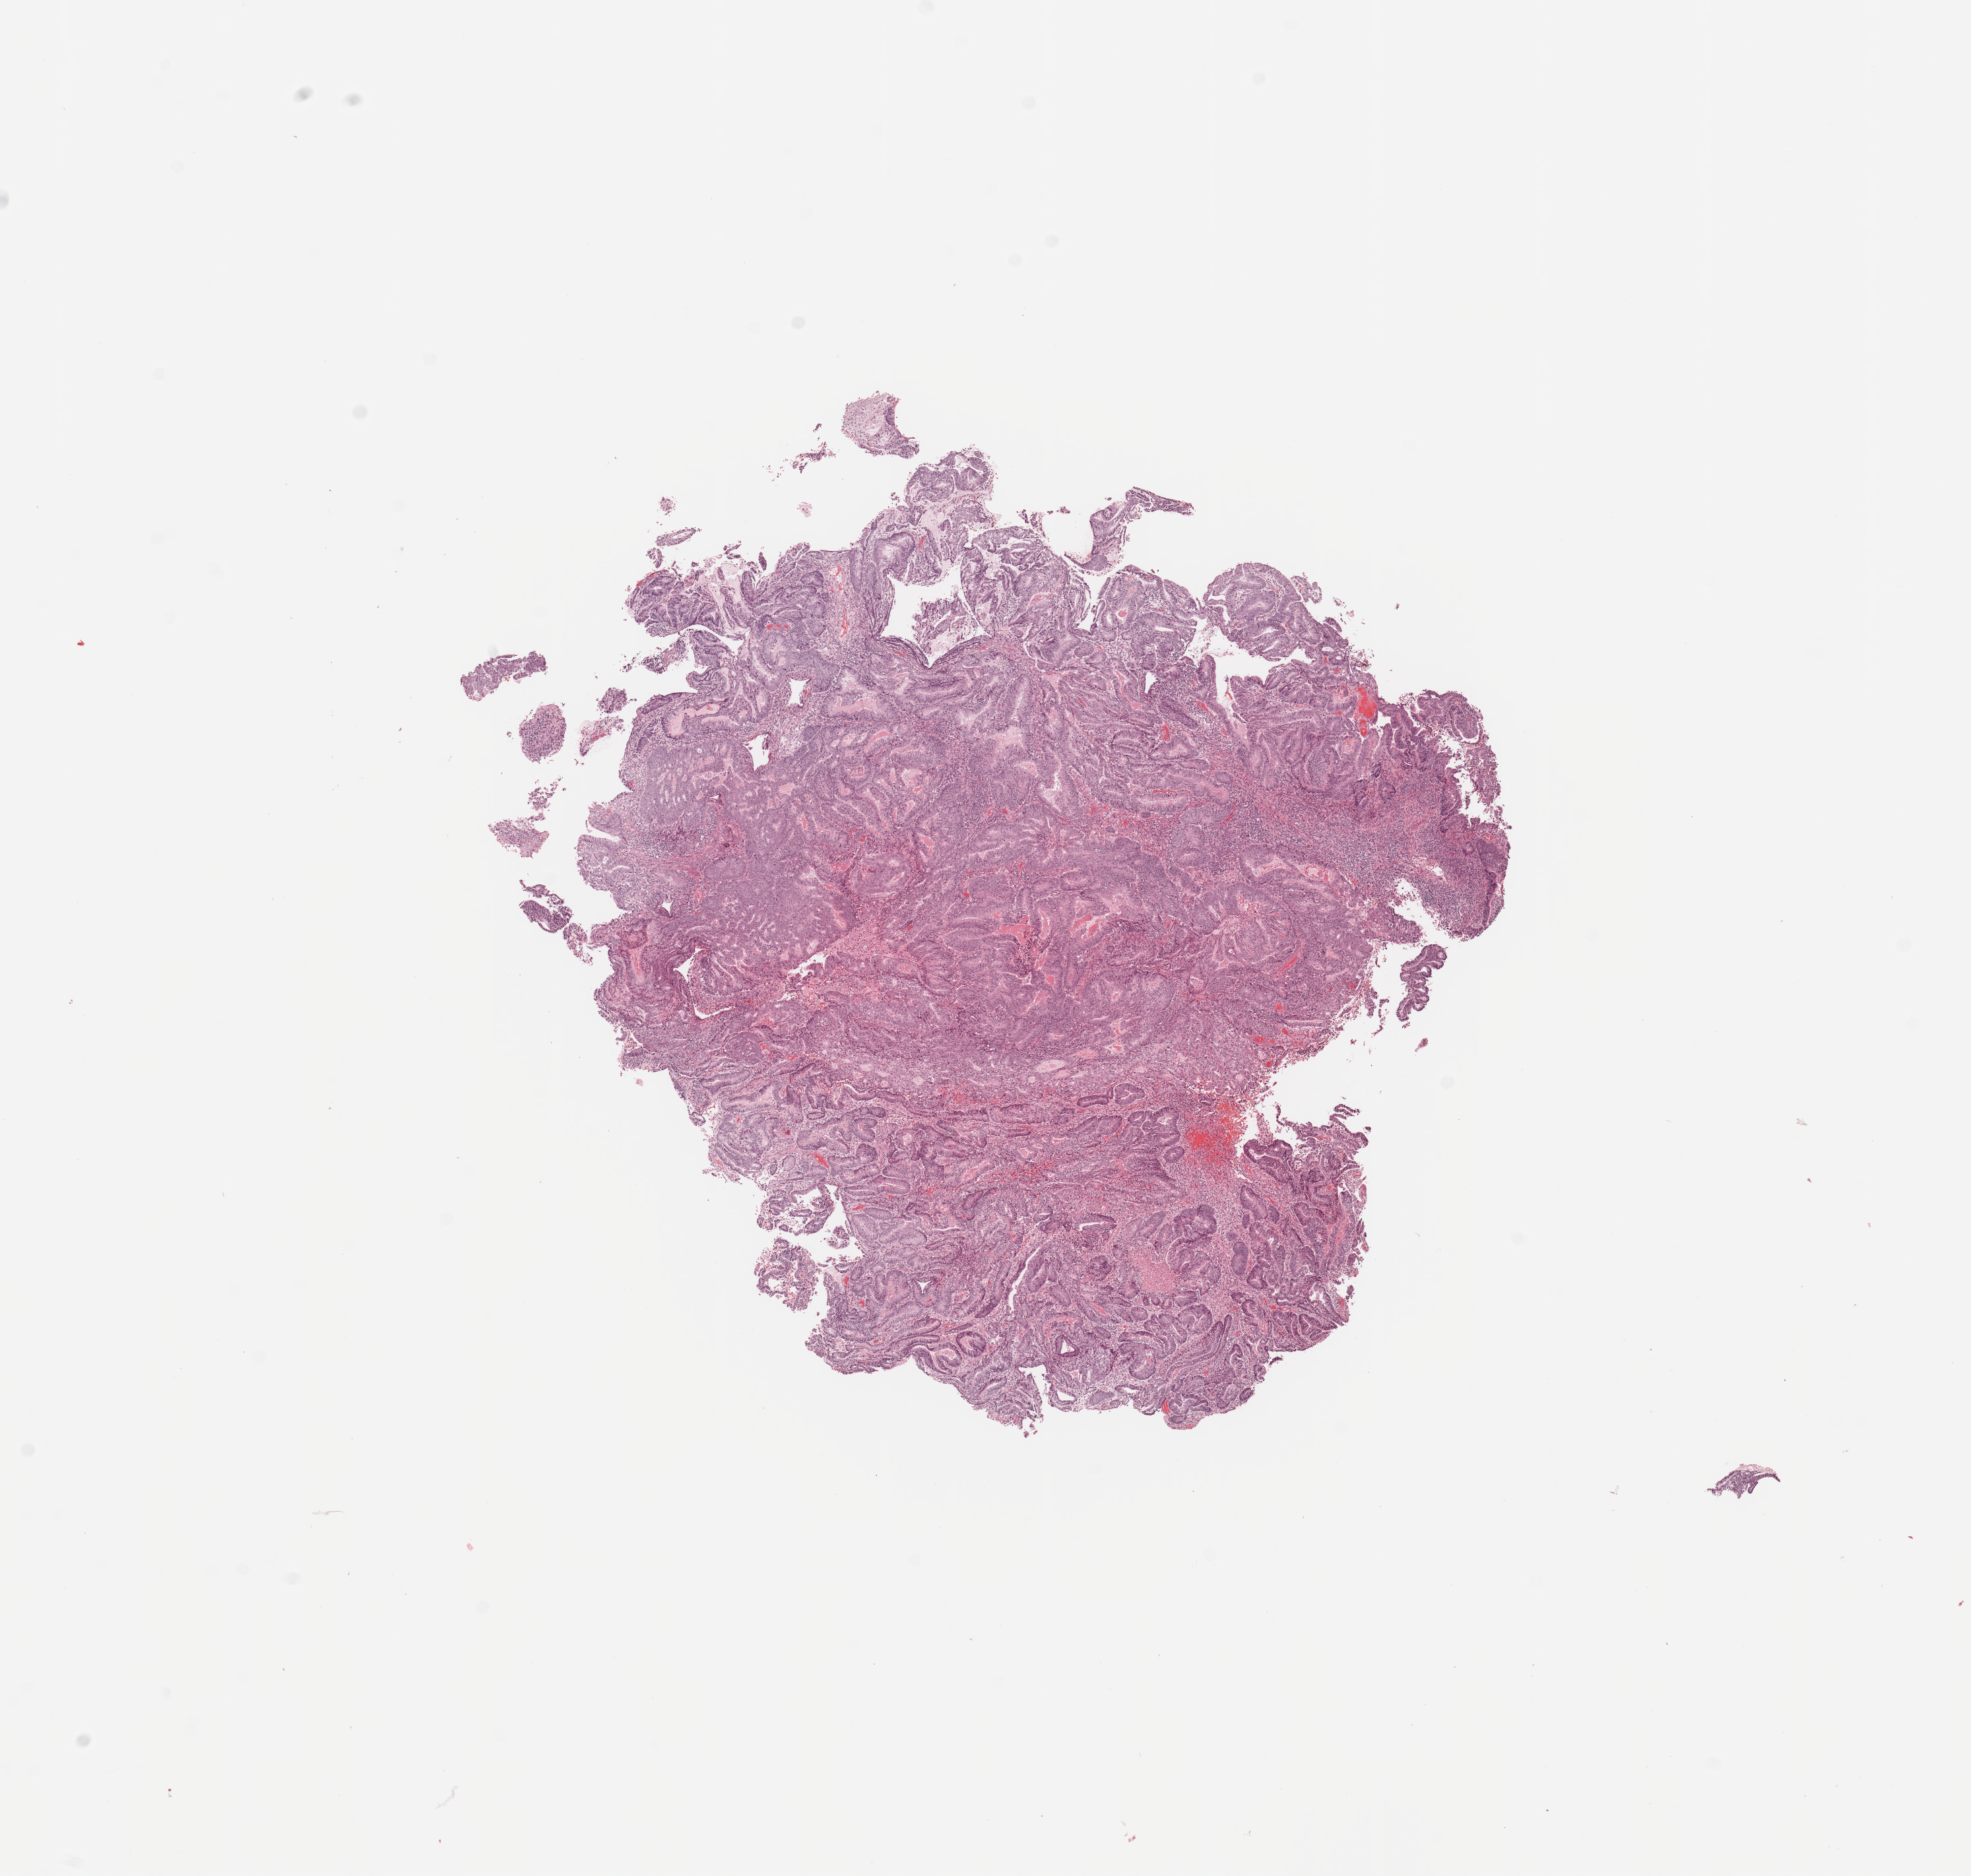
H&E-stained whole-slide image — shown as a low-resolution overview of the whole scanned area (about 11.8 x 11.2 mm); tumour tissue sample, sampled site: uterus. Patient: female, age 71 years. Histologic grade: G1 (well differentiated). Composition of this section per pathologist review: tumour nuclei 85%, necrosis 2%.
AJCC pathologic stage: I. Diagnosis: Endometrioid adenocarcinoma, NOS.